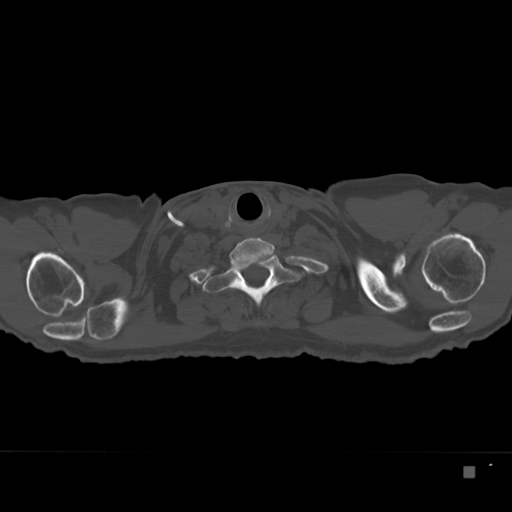
CT including the spine, one axial slice; position 319 of 332 along the scan axis; reconstruction kernel Br40s; 120 kVp; bone window (W 1800 / L 400 HU); 1.5 mm slice thickness; 512 × 512 image matrix, field of view 389 × 389 mm. Patient: male, 72 years. From the clinical record (not read from this slice): primary cancer: skeletal.
Structures marked on this image (semi-automatic segmentation, software-assisted and operator-edited):
- T1 vertebra: bounding box <202,253,306,307> (left, top, right, bottom; pixels)